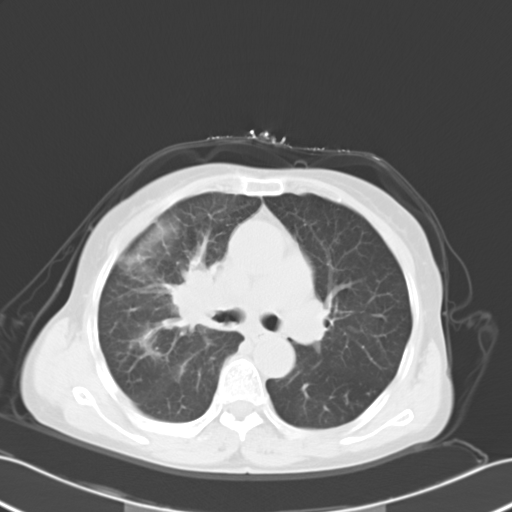
Chest CT, one axial slice; position 17 of 27 along the scan axis; reconstruction kernel B40f; lung window (W 1500 / L -600 HU); 10 mm slice thickness; 512 × 512 image matrix, field of view 353 × 353 mm. Patient: female, 67 years. Case-level facts recorded for this patient, not image findings: clinical TNM (as recorded): T2a N3 M0; histopathological grade: G3.
Structures marked on this image (rectangle marked by the reading radiologist):
- lung tumour (recorded histology: small cell carcinoma): bounding box <159,249,222,335> (left, top, right, bottom; pixels)